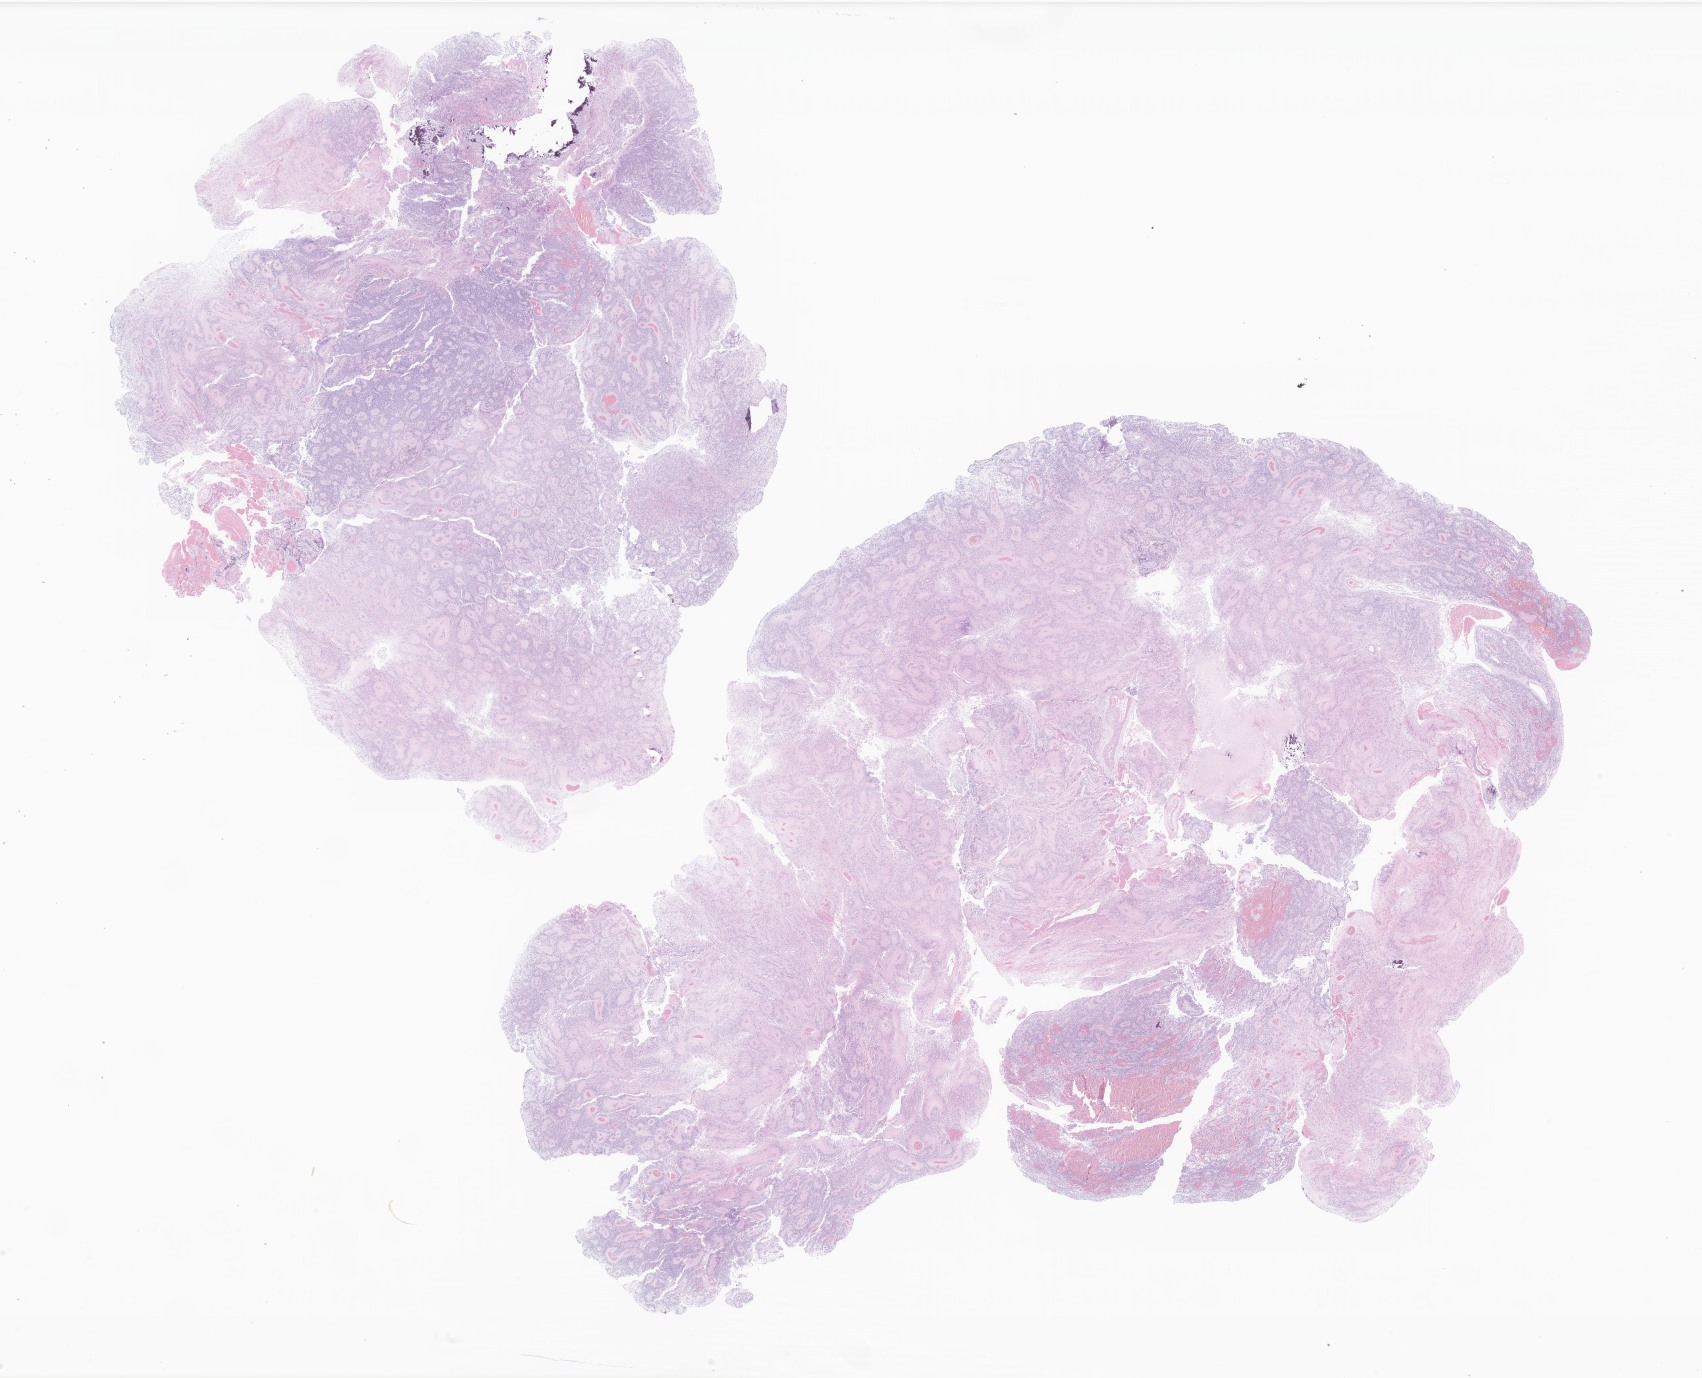
Whole-slide image, H&E stain of tumor tissue from the cerebellum, whole scanned area (about 28.7 x 23.2 mm) shown as a low-resolution overview, FFPE section. Male patient, age 596 days.
- diagnosis: Ependymoma, NOS